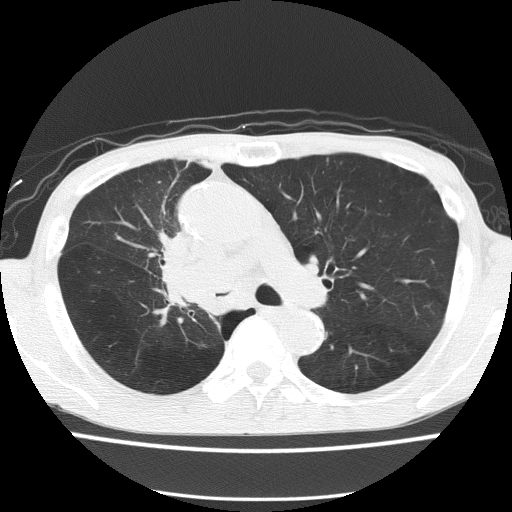
Low-dose screening chest CT, one axial slice; position 95 of 150 along the scan axis; reconstruction kernel FC51; 120 kVp; lung window (W 1500 / L -600 HU); 512 × 512 image matrix.
Annotated regions visible in this slice (outlined manually by an expert reader):
- lesion 1 (tumor, hilum of right lung): box from (x=166, y=232) to (x=226, y=315) px